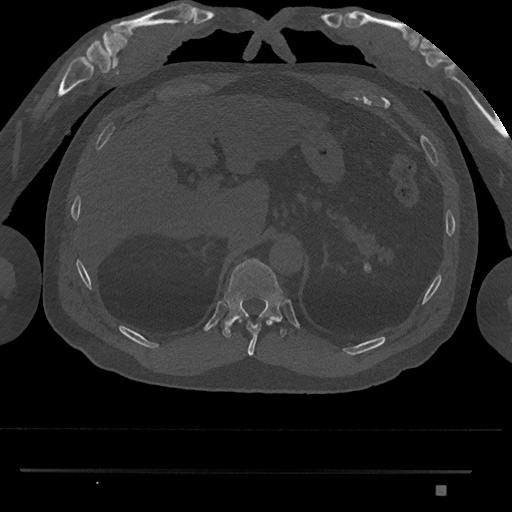
CT including the spine, one axial slice. Reconstruction kernel Br40s/3. 120 kVp. Bone window (W 1800 / L 400 HU). 512 × 512 image matrix, field of view 429 × 429 mm. Male patient, age 65 years. From the clinical record (not read from this slice): primary cancer: prostate.
Structures marked on this image (semi-automatic segmentation, software-assisted and operator-edited):
- T10 vertebra: bounding box [x1, y1, x2, y2] px = [238, 319, 272, 356]
- T11 vertebra: [221, 258, 287, 338]